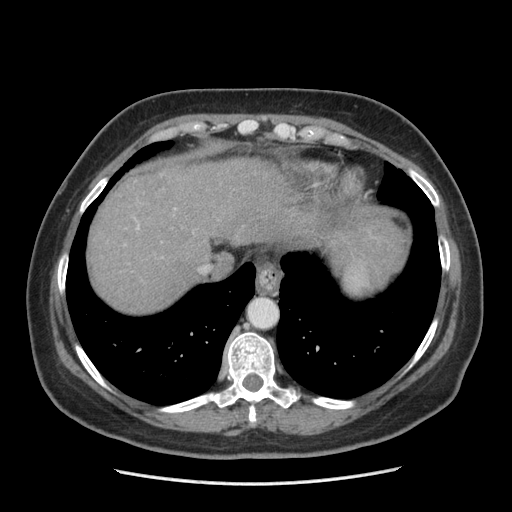
Contrast-enhanced abdominal CT (liver protocol), one axial slice. Slice 169 of 185 in the series (ordered by position). Reconstruction kernel STANDARD. 140 kVp. Soft-tissue window (W 400 / L 40 HU). 512 × 512 image matrix, field of view 360 × 360 mm. Case-level facts recorded for this patient, not image findings: diagnosis: hepatocellular carcinoma (patient treated with transarterial chemoembolisation; whether this scan precedes or follows treatment is not stated here); TNM stage (as recorded): Stage-I; Child-Pugh class: A.
Annotated regions visible in this slice (semi-automatic segmentation, software-assisted and operator-edited):
- liver parenchyma outside the tumour (the mass and vessels are separate outlines, so this box may not span the whole liver): bounding box [x1, y1, x2, y2] px = [88, 158, 407, 312]